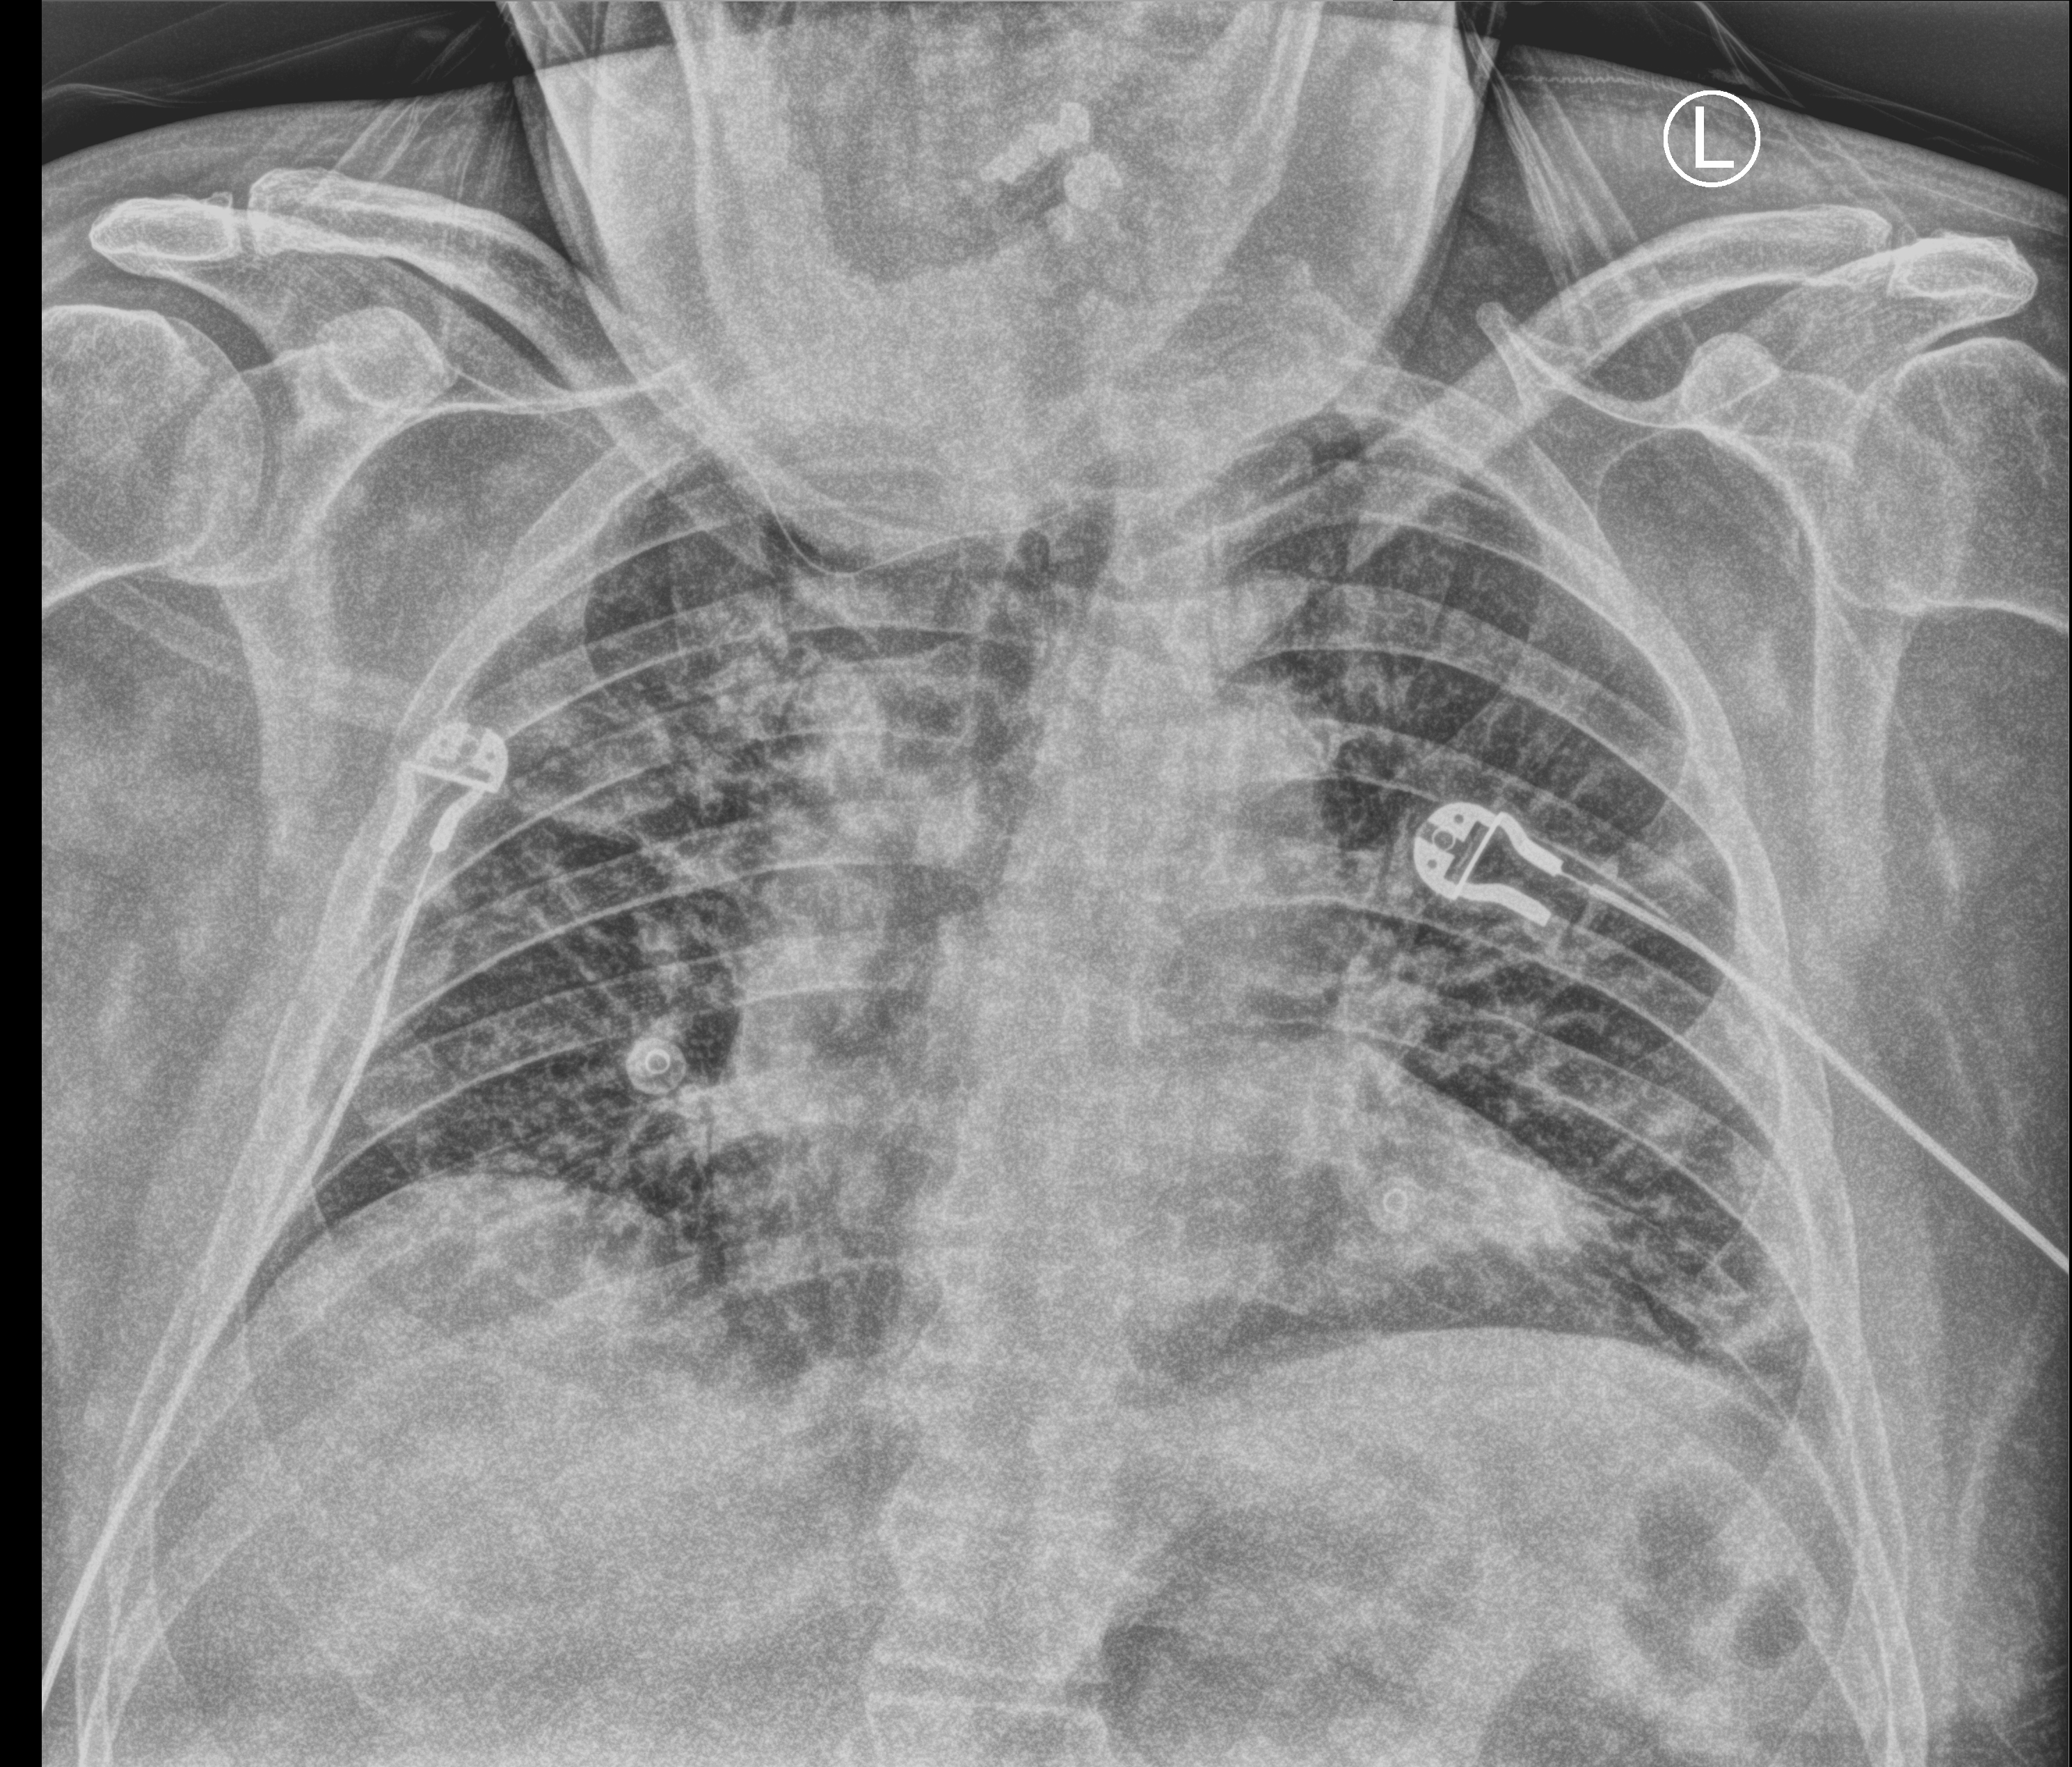
Bedside chest radiograph (computed radiography). Male patient hospitalised with COVID-19, age 60–74 years.
From the hospital-stay record, not from the radiograph (when in the stay this image was taken is not recorded): admitted to intensive care during this hospital stay: no; length of hospital stay: 6 days; mechanically ventilated during this hospital stay: no.